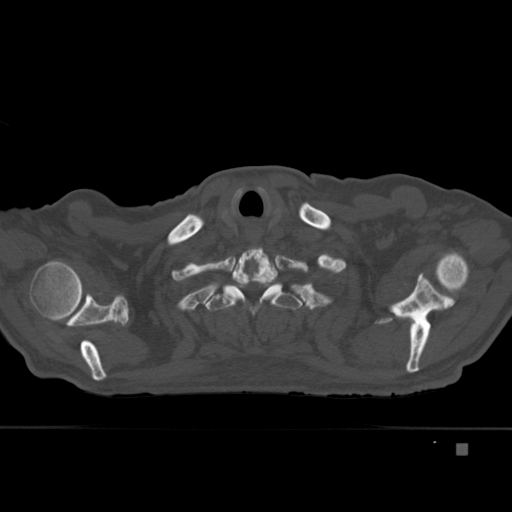
CT including the spine, one axial slice; slice 353 of 451 in the series (ordered by position); bone window (W 1800 / L 400 HU); 1.5 mm slice thickness; 512 × 512 image matrix, field of view 378 × 378 mm. Male patient, age 75 years. Case-level facts recorded for this patient, not image findings: primary cancer: prostate.
Annotated regions visible in this slice (semi-automatically segmented with operator editing):
- T1 vertebra: bounding box <223,247,283,303> (left, top, right, bottom; pixels)
- T2 vertebra: <203,283,303,315>